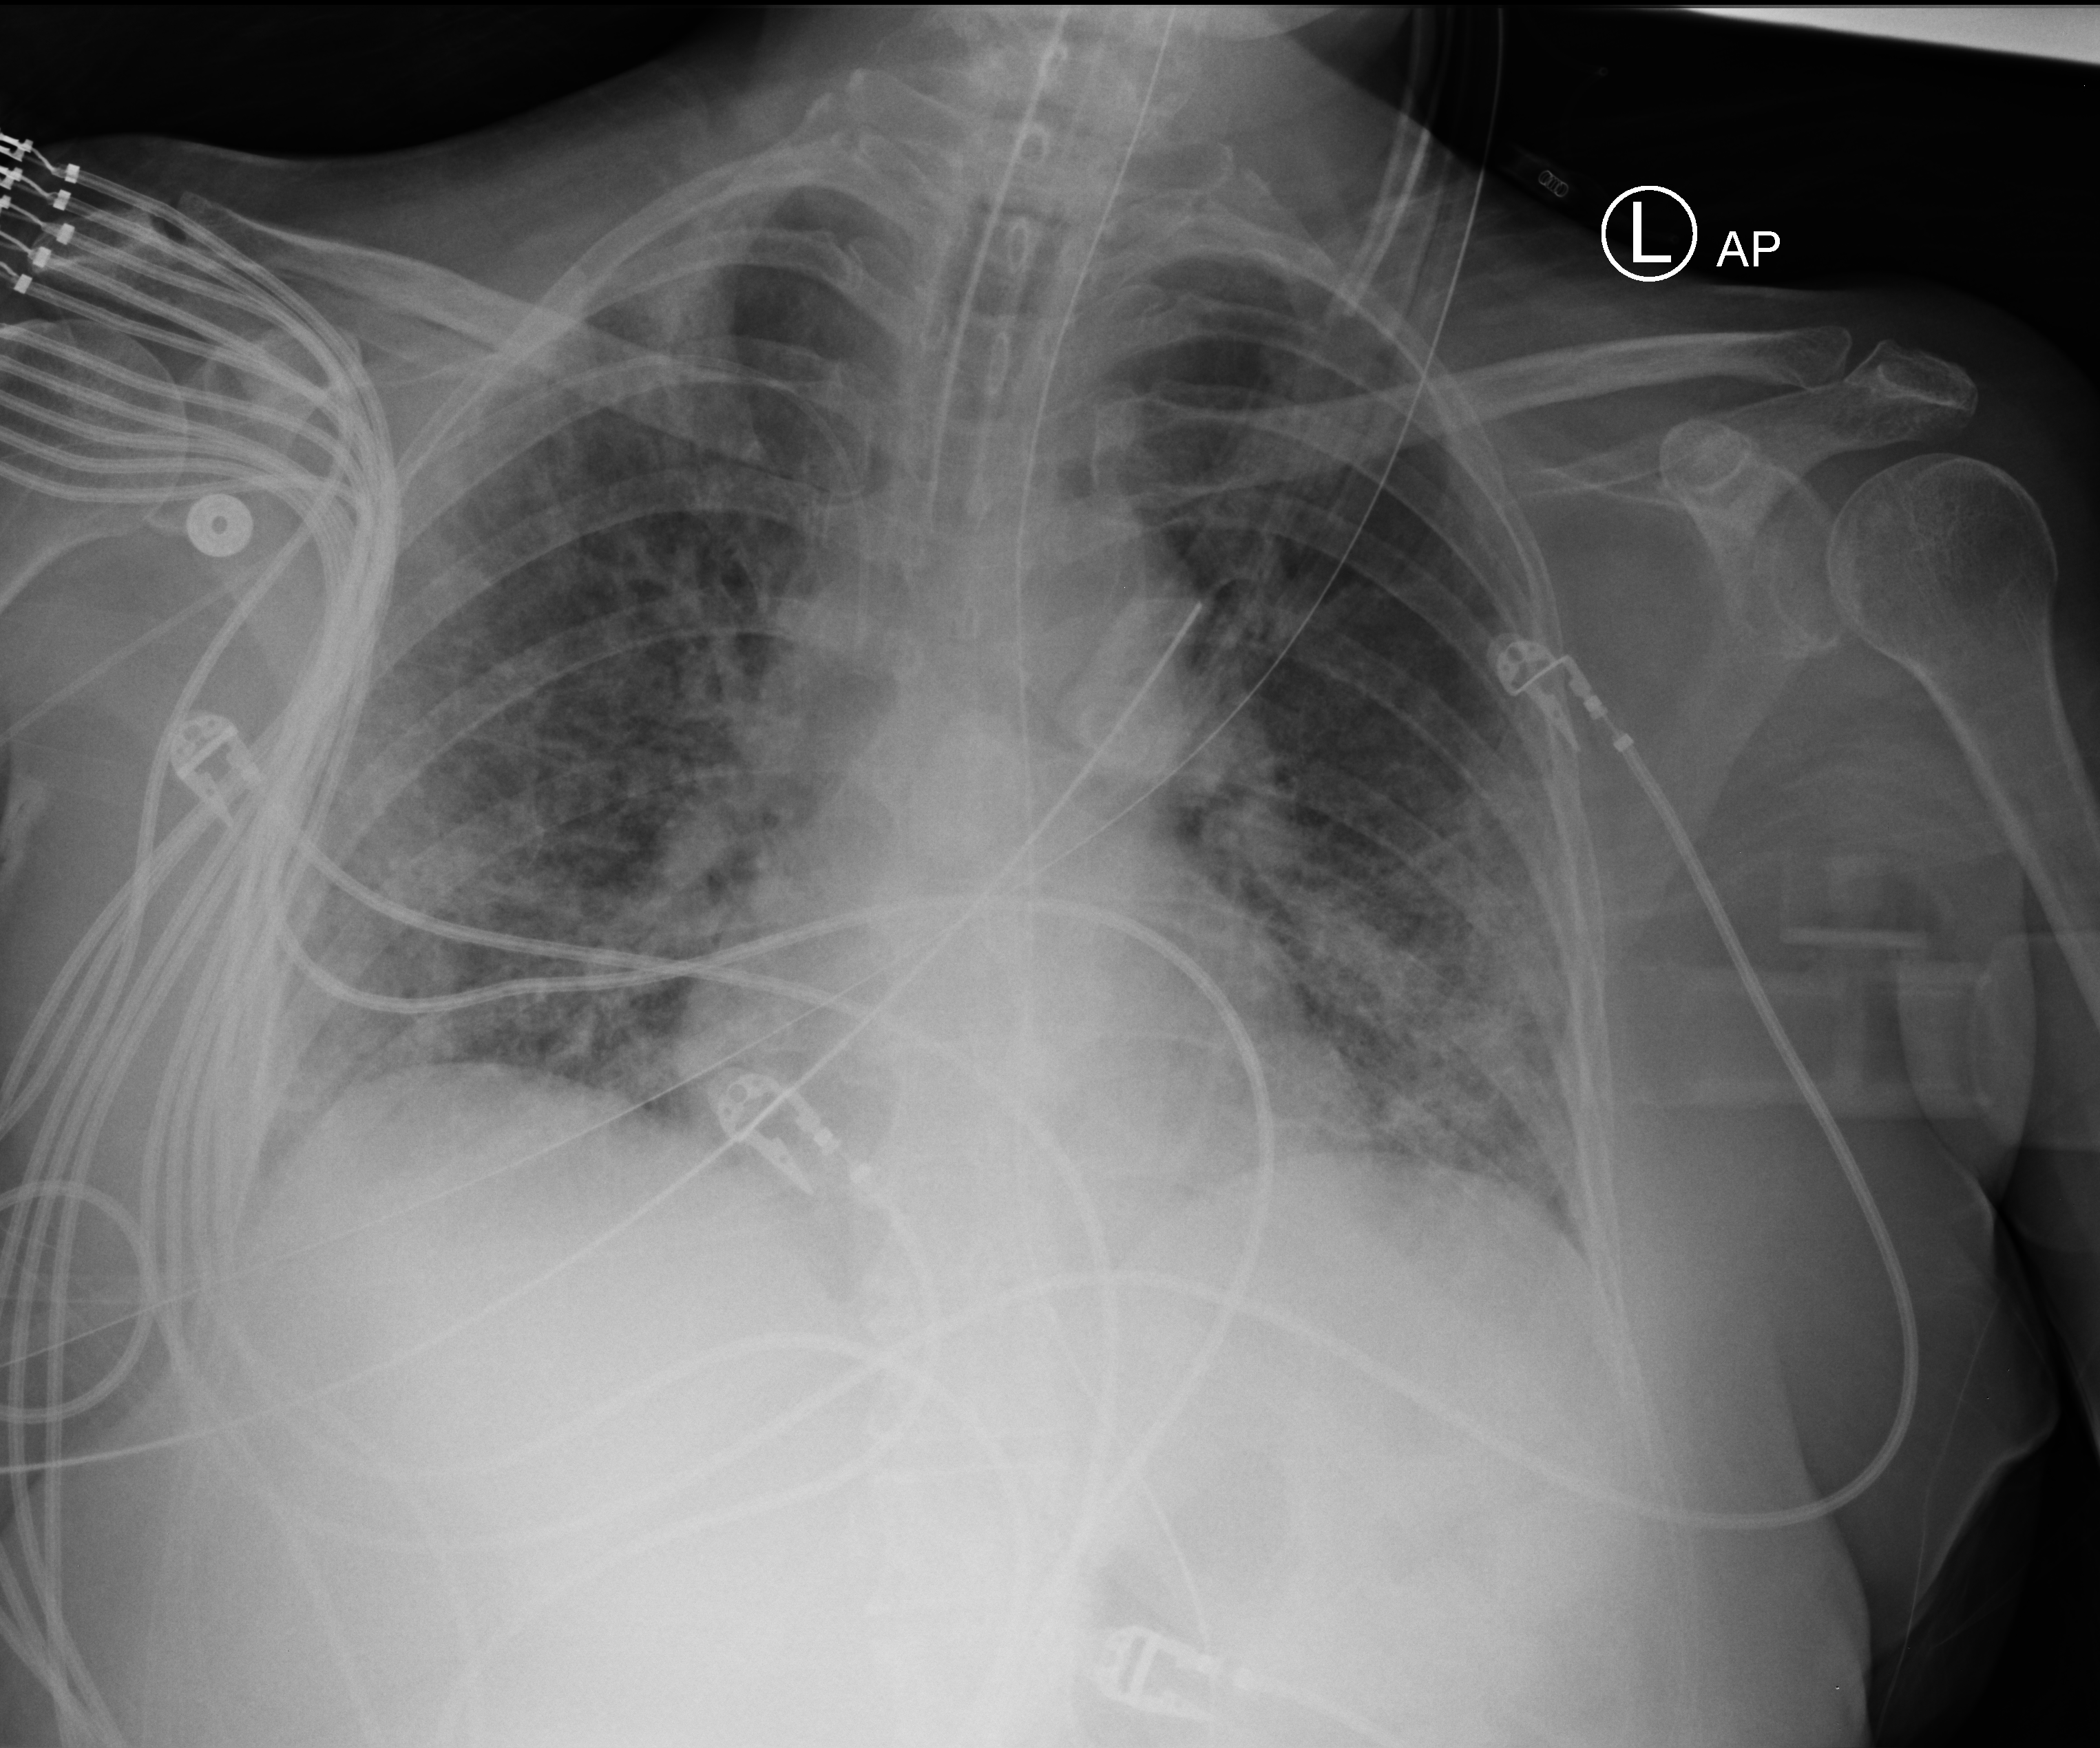
Chest X-ray (portable). Female patient hospitalised with COVID-19, age 60–74 years.
Admission-level facts for this patient (not findings on this image; timing relative to this image not recorded): hypertension (admission record): yes; mechanically ventilated during this hospital stay: yes.